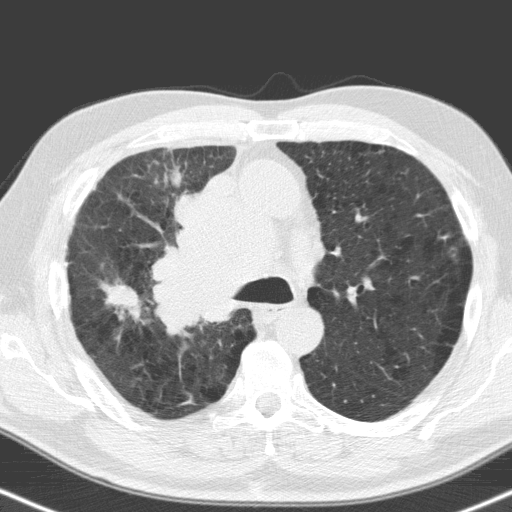
Low-dose screening chest CT, one axial slice. Position 111 of 160 along the scan axis. Lung window (W 1500 / L -600 HU). 3.2 mm slice thickness. 512 × 512 image matrix, field of view 324 × 324 mm.
Outlined on this slice (expert manual segmentation):
- lesion 1 (tumor, hilum of right lung): box from (x=154, y=177) to (x=265, y=327) px
- lesion 2 (tumor, upper lobe of right lung): (x=109, y=284)–(x=140, y=308)